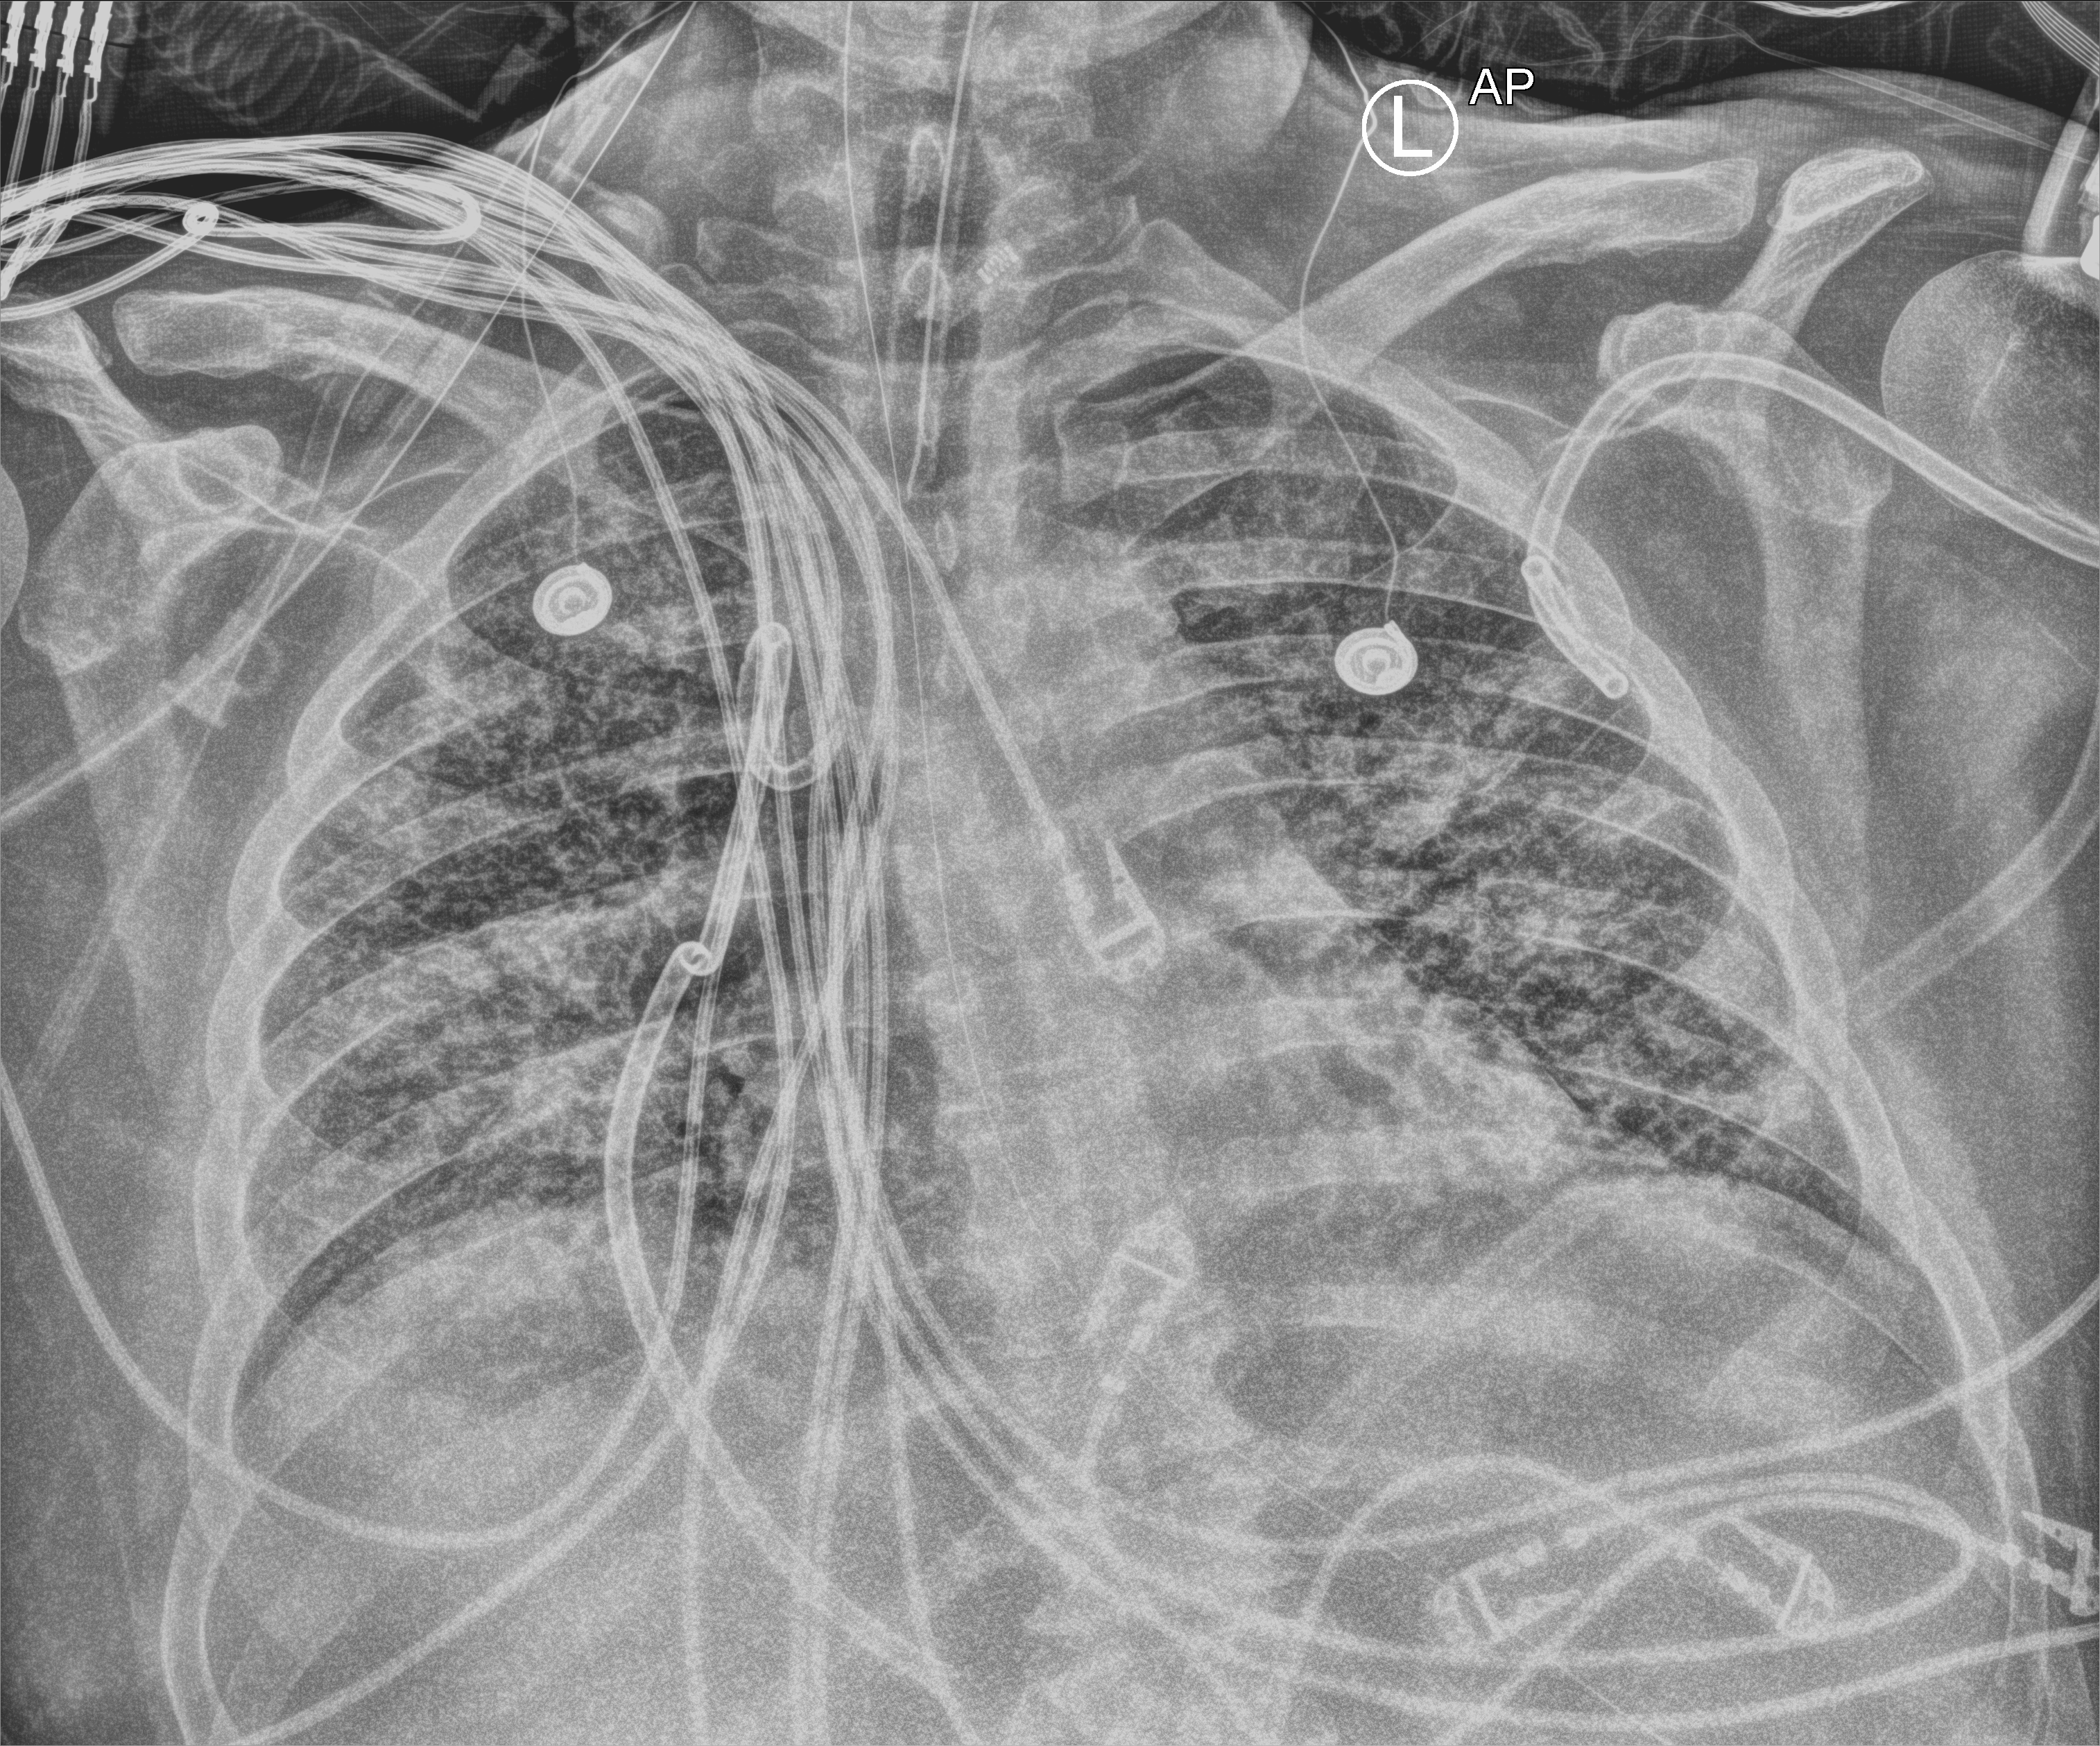
Bedside chest radiograph (computed radiography); anteroposterior (AP) projection. Adult patient hospitalised with COVID-19, age 18–59 years.
From the hospital-stay record, not from the radiograph (when in the stay this image was taken is not recorded): length of hospital stay: 31 days.